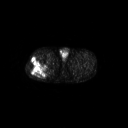
FDG PET of an extremity soft-tissue mass (from a PET/CT study), one axial slice; position 262 of 267 along the scan axis; 128 × 128 image matrix, field of view 700 × 700 mm. Patient: male, 43 years. Case-level facts recorded for this patient, not image findings: histological type: poorly differentiated synovial sarcoma; grade: high; site of the primary tumour: right buttock.
Outlined on this slice (expert contour drawn on MRI and transferred to this co-registered scan by the dataset authors):
- gross tumour volume including surrounding oedema: bounding box <28,58,50,78> (left, top, right, bottom; pixels)
- gross tumour volume (mass): <28,58,48,78>